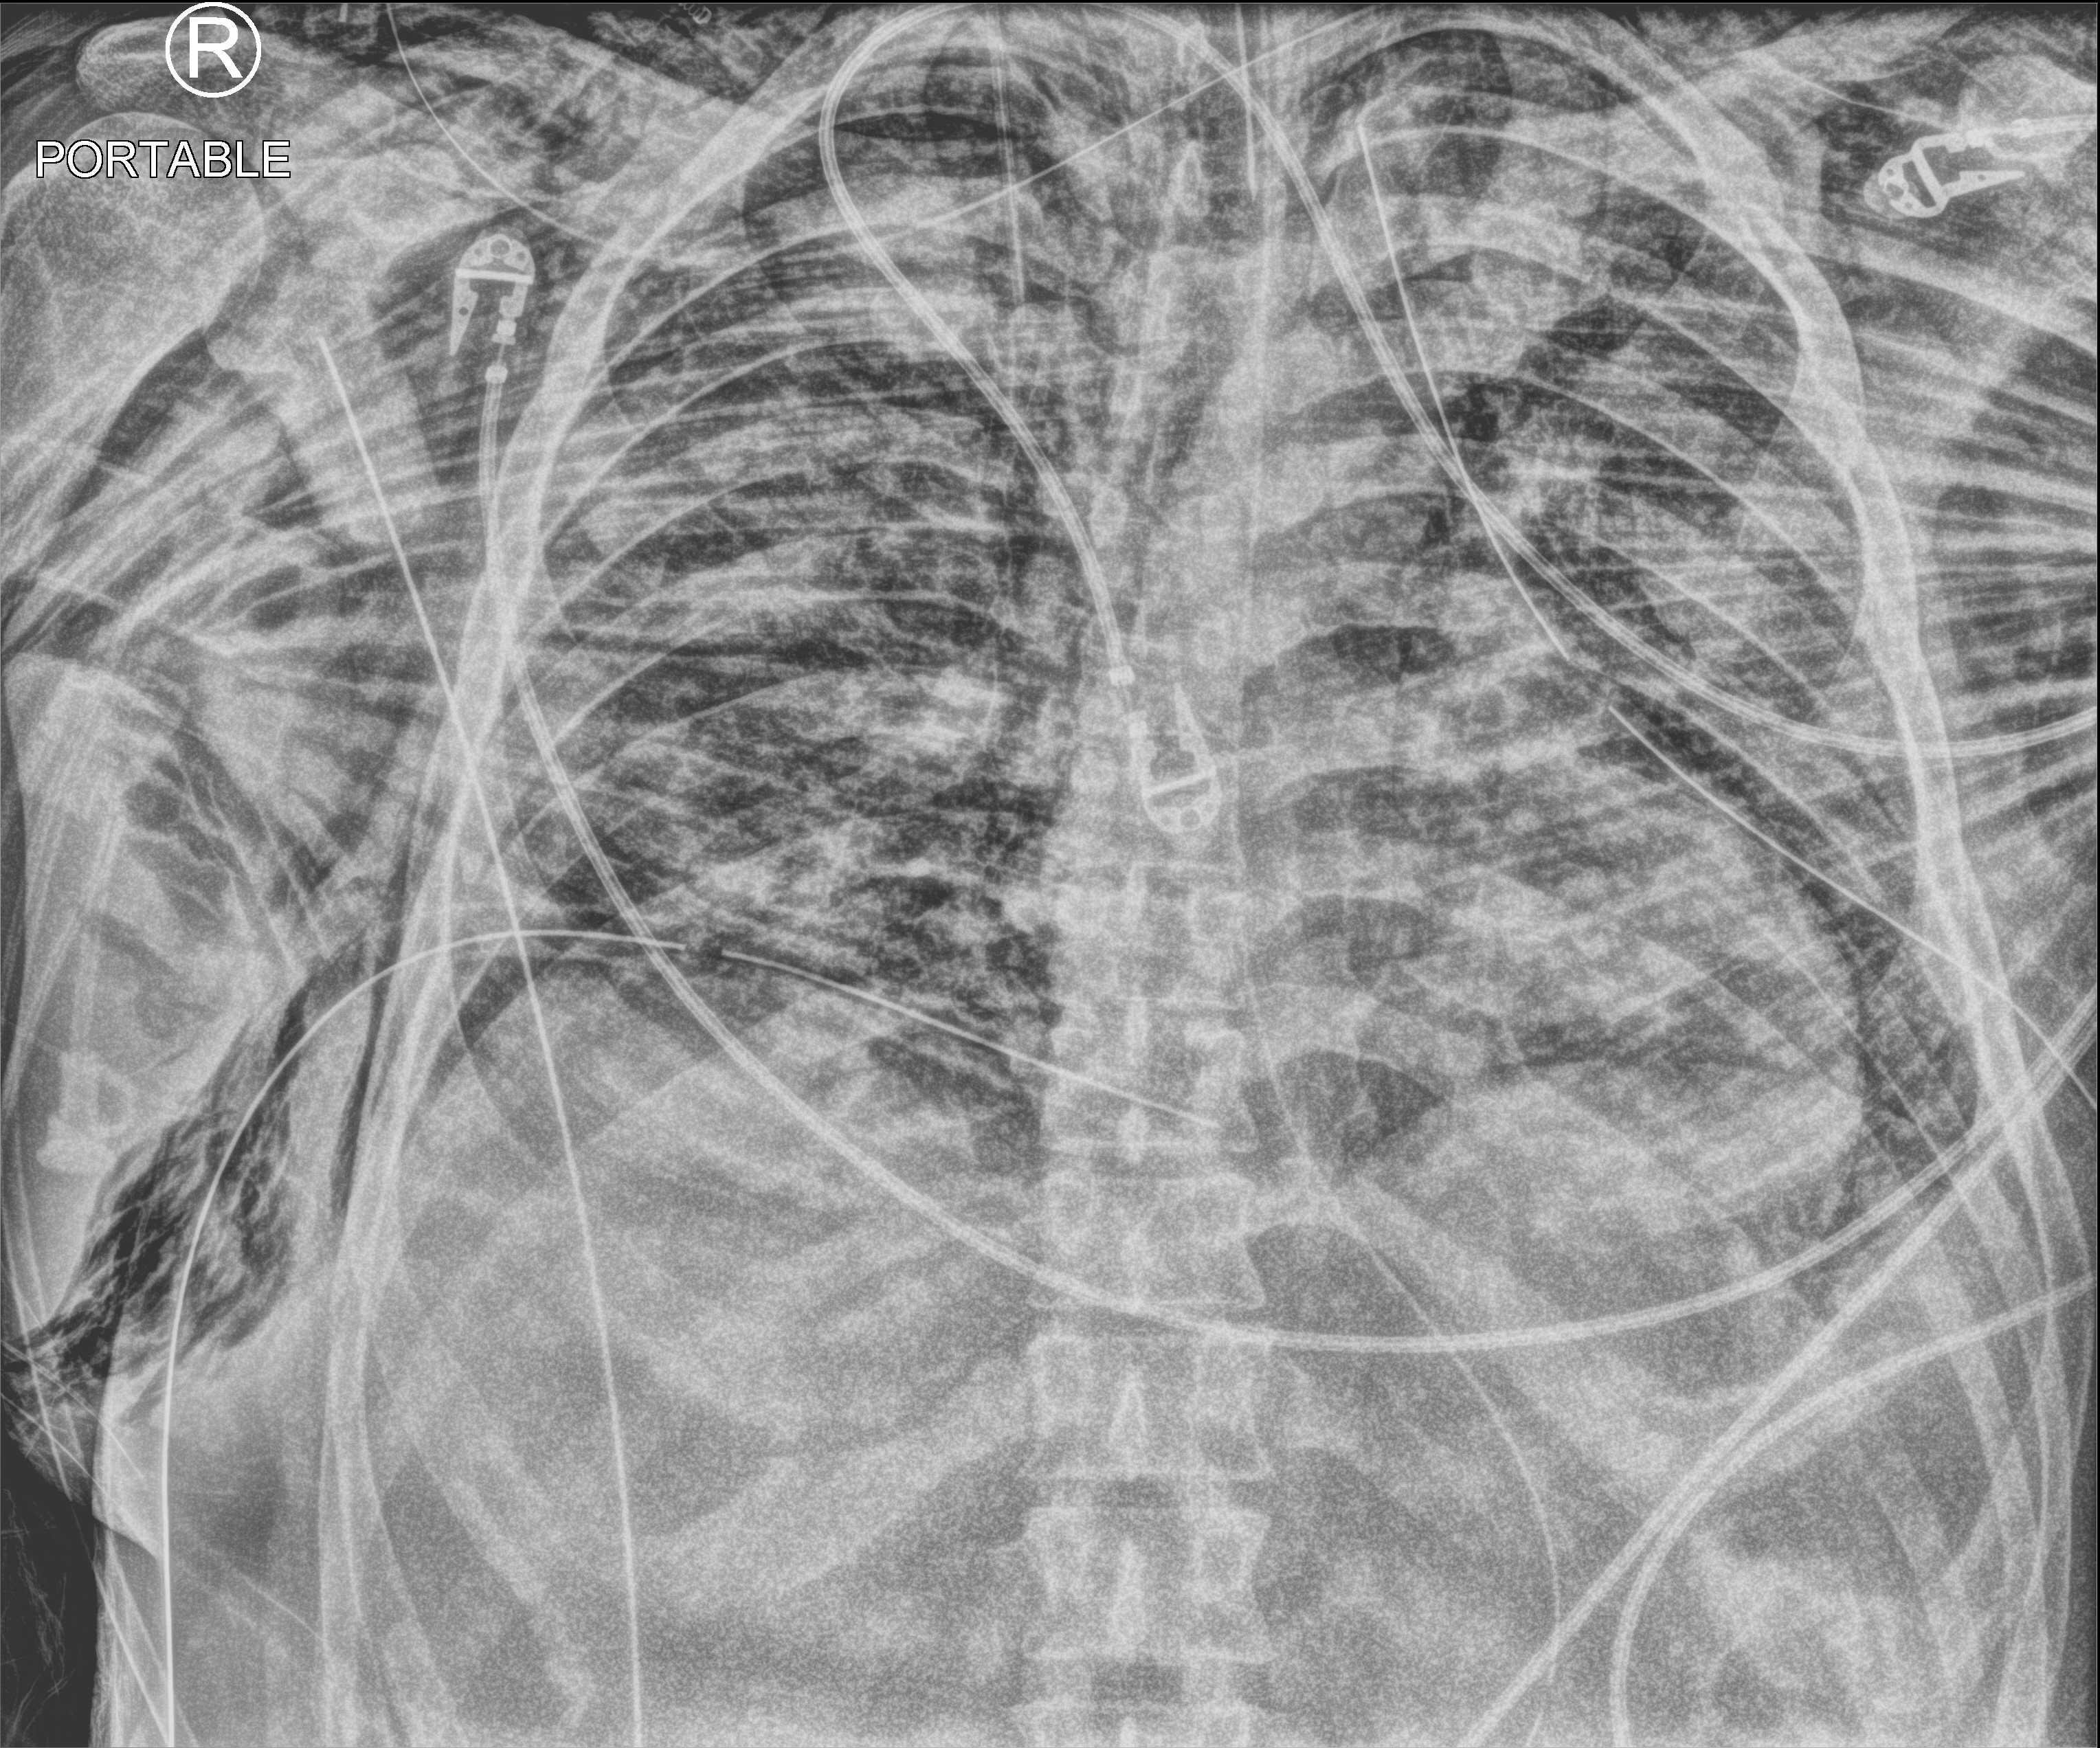
Bedside chest radiograph (computed radiography); anteroposterior (AP) projection. Patient hospitalised with COVID-19; male, aged 18–59 years.
Hospital-stay facts (about this admission, not read from this image; timing relative to this image not recorded): length of hospital stay: 29 days; mechanically ventilated during this hospital stay: yes; admitted to intensive care during this hospital stay: yes.